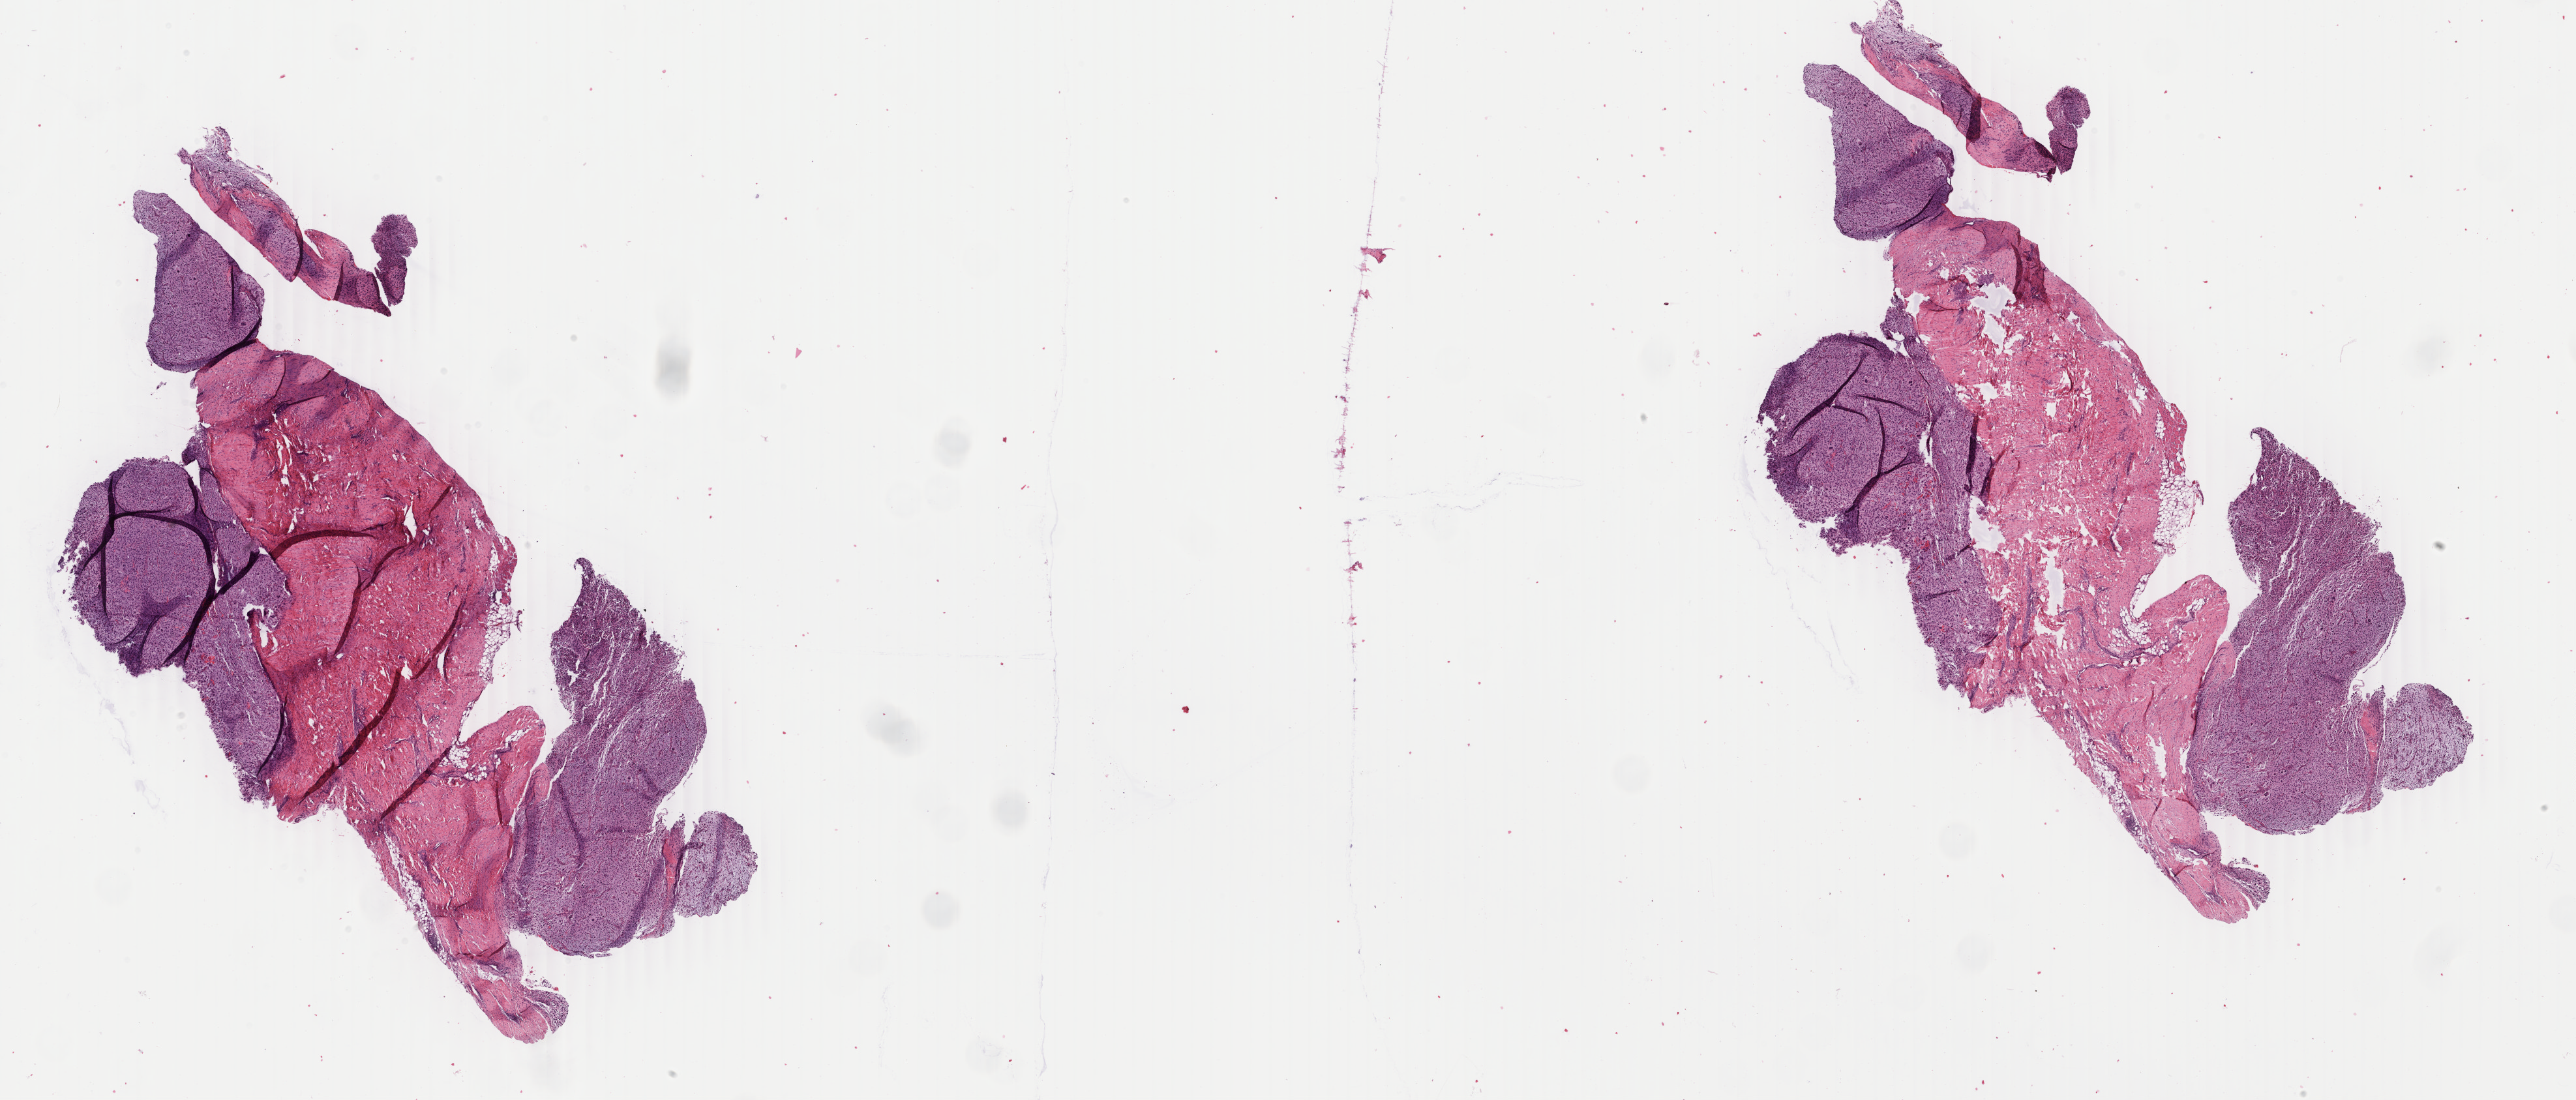
Whole-slide histology image, Hematoxylin and eosin (H&E) stained, whole scanned area (about 31.4 x 13.4 mm, from a 40x scan) shown as a low-resolution overview; formalin-fixed paraffin-embedded (FFPE) diagnostic section; primary tumour sample from the connective, subcutaneous and other soft tissues. Patient: female, age at initial diagnosis 65 years.
Histologic diagnosis: Undifferentiated sarcoma (connective, subcutaneous and other soft tissues of pelvis).